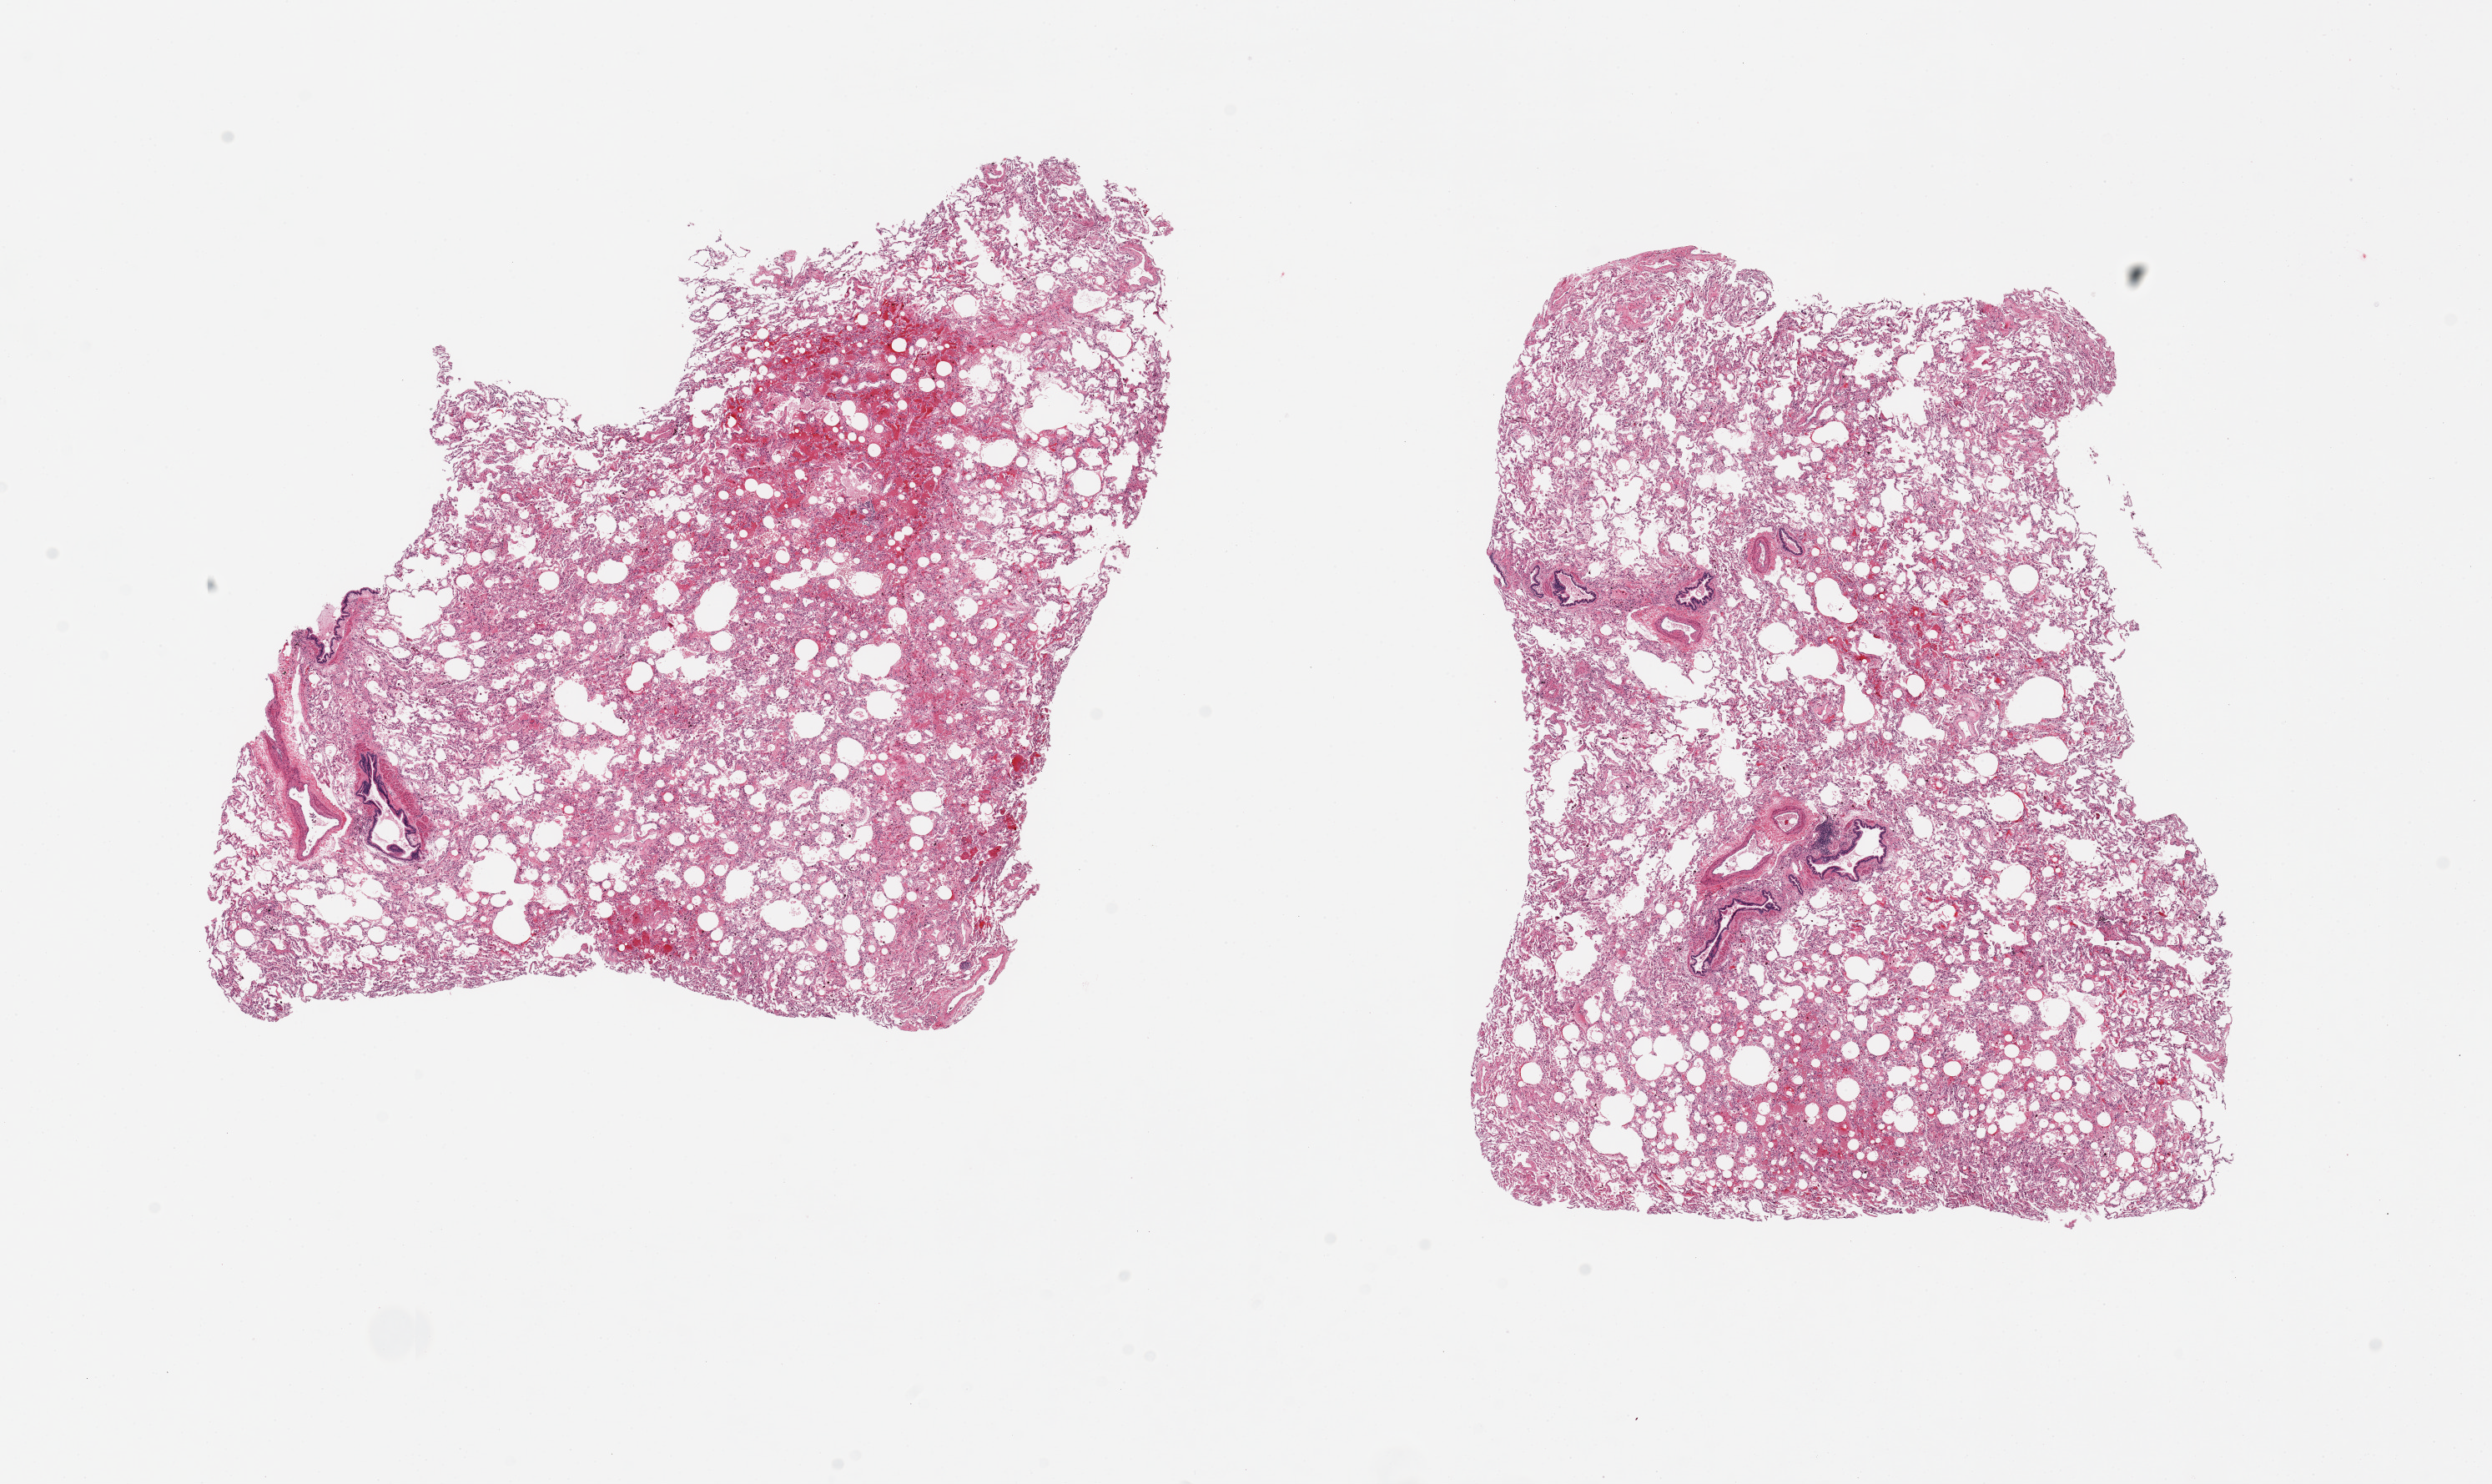
Hematoxylin and eosin (H&E) whole-slide image, brightfield, whole scanned area (about 23.6 x 14.1 mm, slide scanned at 20x) shown as a low-resolution overview; PAXgene-fixed paraffin-embedded (PFPE) section; target tissue: lung; tissue donor sample. Female donor.
Review note (as recorded): 2 pieces. 11x8 & 9x7mm; Patchy alveolar hemorrhage.